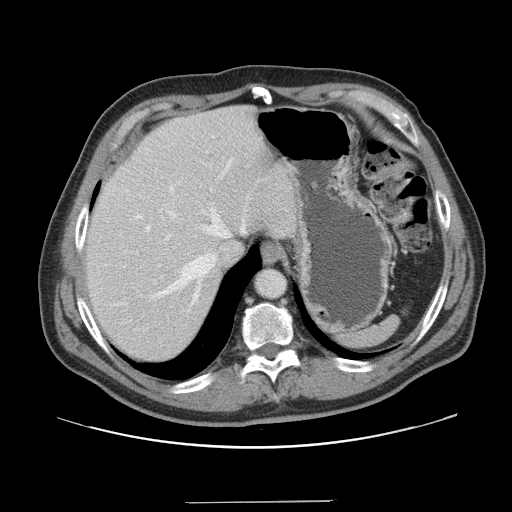
Contrast-enhanced abdominal CT, one axial slice; slice 126 of 151 in the series (ordered by position); 120 kVp; intravenous contrast given; soft-tissue window (W 400 / L 40 HU); 2.5 mm slice thickness; 512 × 512 image matrix. Male patient, age 63 years. Case-level facts recorded for this patient, not image findings: diagnosis: colorectal cancer liver metastases, imaged before liver resection; multiple liver metastases: no; largest metastasis: 2.1 cm; disease in both lobes: no.
Outlined on this slice (expert manual segmentation):
- hepatic veins: box from (x=136, y=159) to (x=245, y=302) px
- liver: (x=85, y=107)–(x=299, y=363)
- planned liver remnant (the part of the liver to remain after resection): (x=85, y=120)–(x=253, y=363)